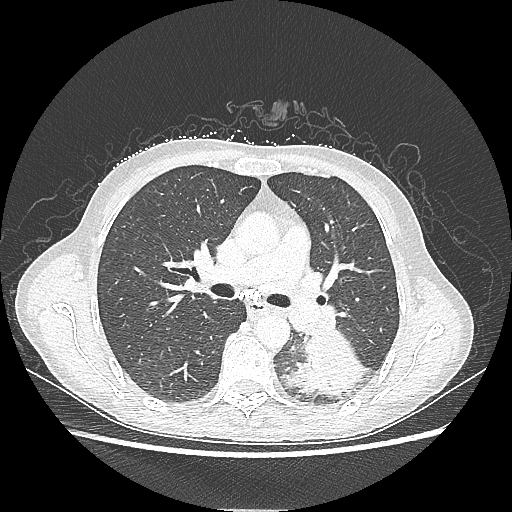
Chest CT, one axial slice; reconstruction kernel LUNG; 80 kVp; lung window (W 1500 / L -600 HU); 512 × 512 image matrix. Female patient, age 53 years. From the clinical record (not read from this slice): clinical TNM (as recorded): T3 N0 M0.
Annotated regions visible in this slice (rectangle marked by the reading radiologist):
- lung tumour (recorded histology: adenocarcinoma): bounding box [x1, y1, x2, y2] px = [287, 336, 368, 401]